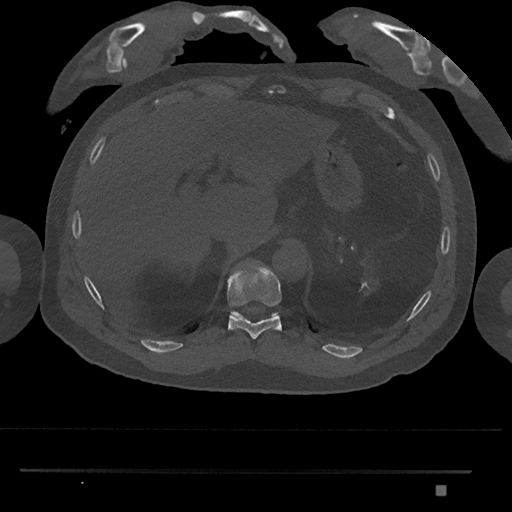
CT including the spine, one axial slice; slice 992 of 1134 in the series (ordered by position); 120 kVp; bone window (W 1800 / L 400 HU); 0.5 mm slice thickness; 512 × 512 image matrix, field of view 429 × 429 mm. Male patient, age 65 years. Case-level facts recorded for this patient, not image findings: primary cancer: prostate.
Structures marked on this image (semi-automatic segmentation, software-assisted and operator-edited):
- T10 vertebra: bounding box [x1, y1, x2, y2] px = [227, 262, 282, 340]
- T11 vertebra: [231, 311, 278, 318]
- T9 vertebra: [251, 352, 254, 356]